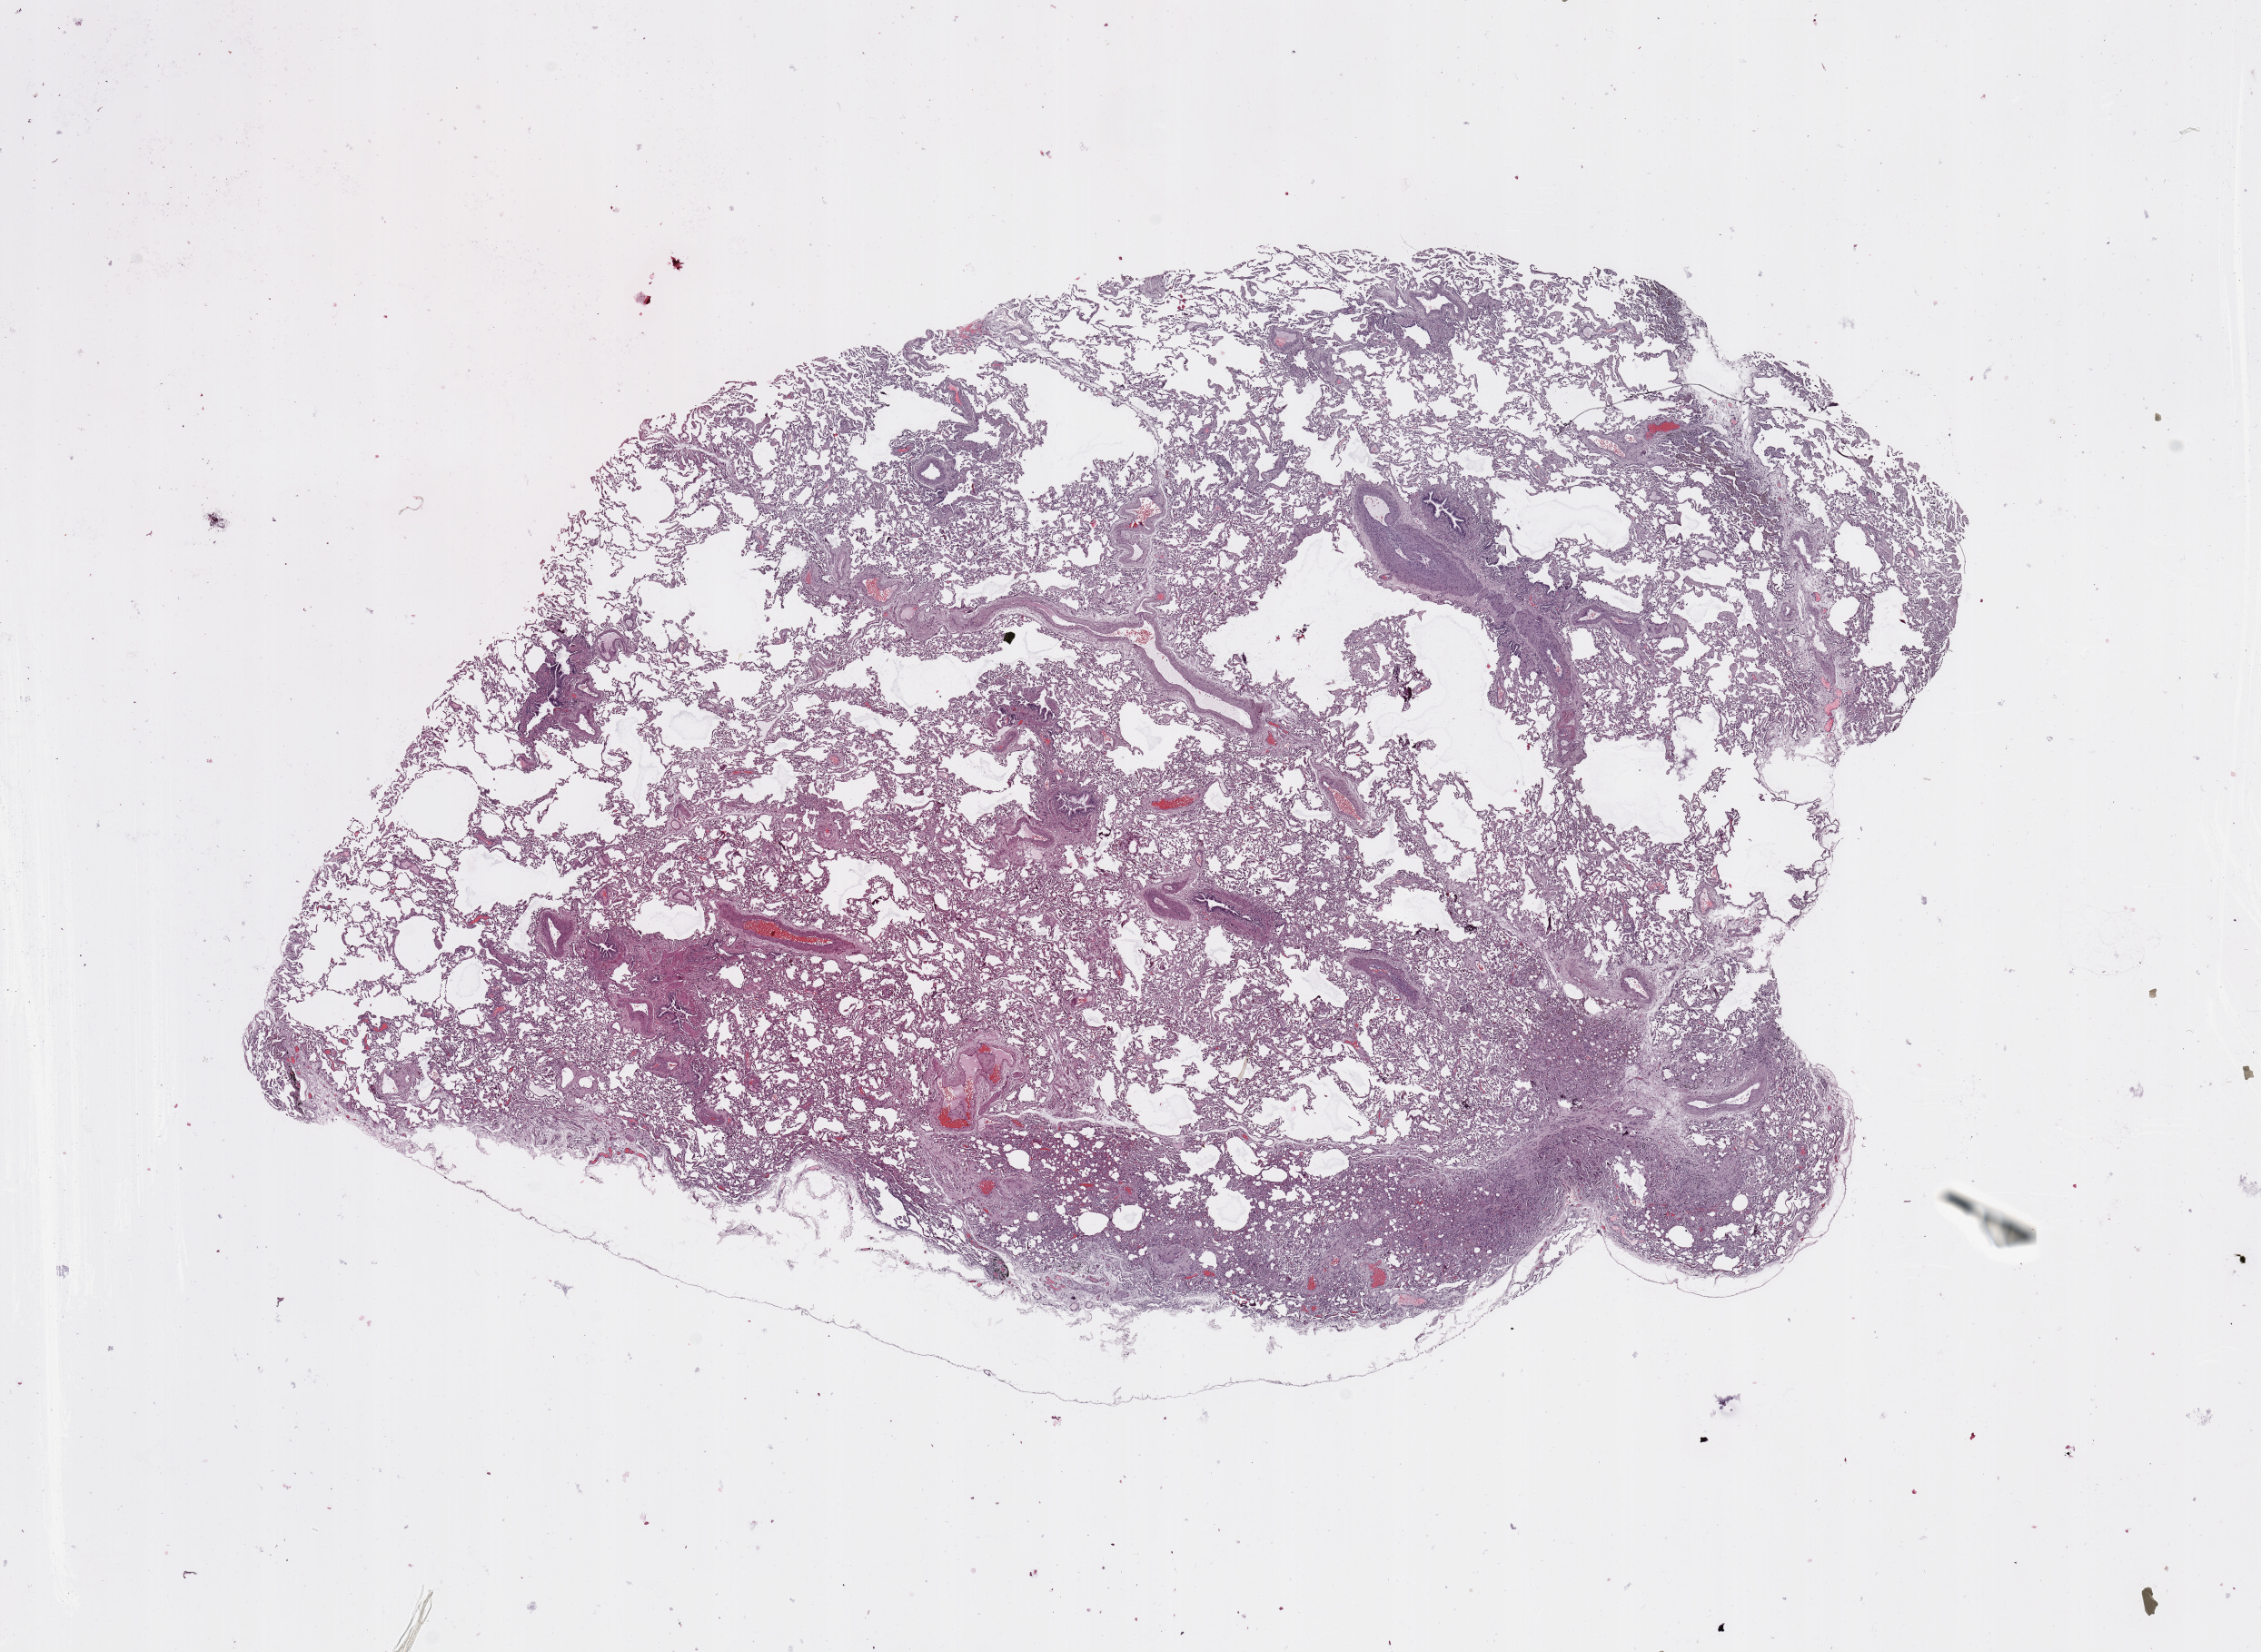
Whole-slide histology image, H&E-stained — low-resolution overview of the scanned area, about 19.7 x 14.4 mm (acquisition: 20x scan). Normal (non-tumour) tissue sample, lung. 64-year-old male patient.
• this section: normal (non-tumour) tissue from the same patient
• patient diagnosis: Adenocarcinoma, NOS